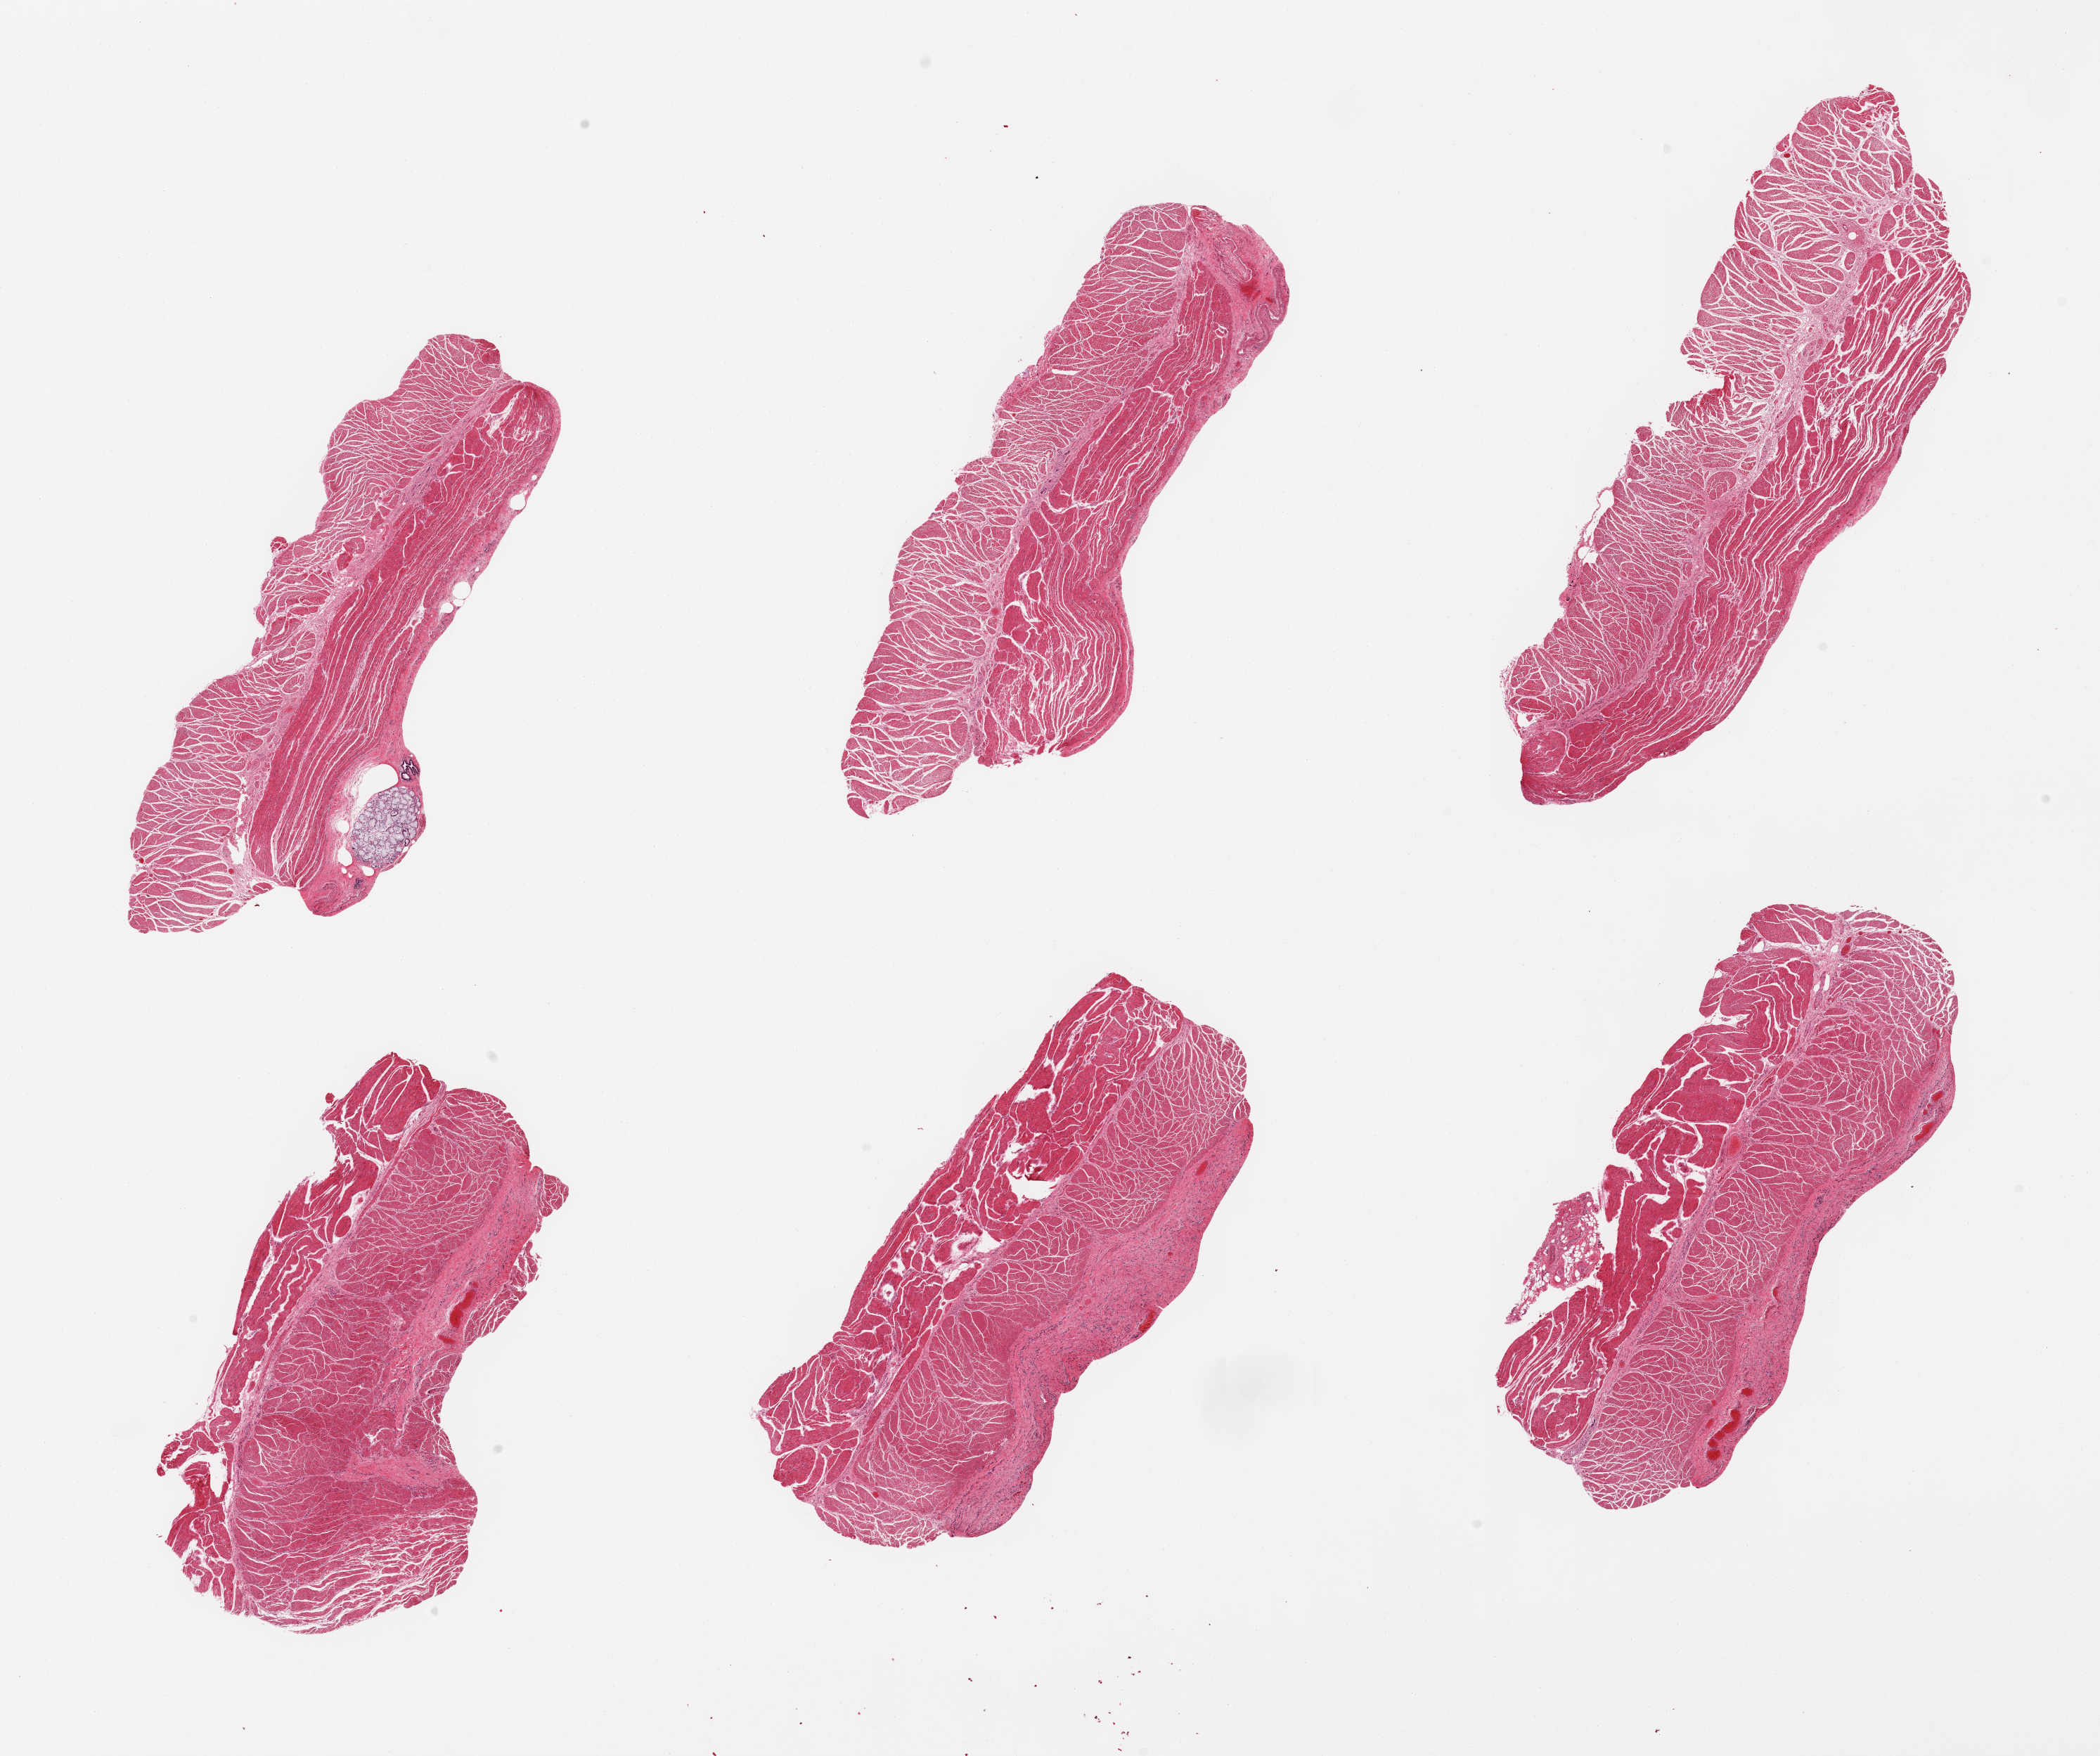
Digitized H&E-stained section, whole scanned area (about 23.6 x 19.8 mm) shown as a low-resolution overview, PAXgene-fixed paraffin-embedded (PFPE) section, target tissue: esophageal muscle, tissue donor sample. Donor sex: male.
Pathologist's review note for this sample: 6 pieces; well trimmed muscle with 1 submucosal gland.